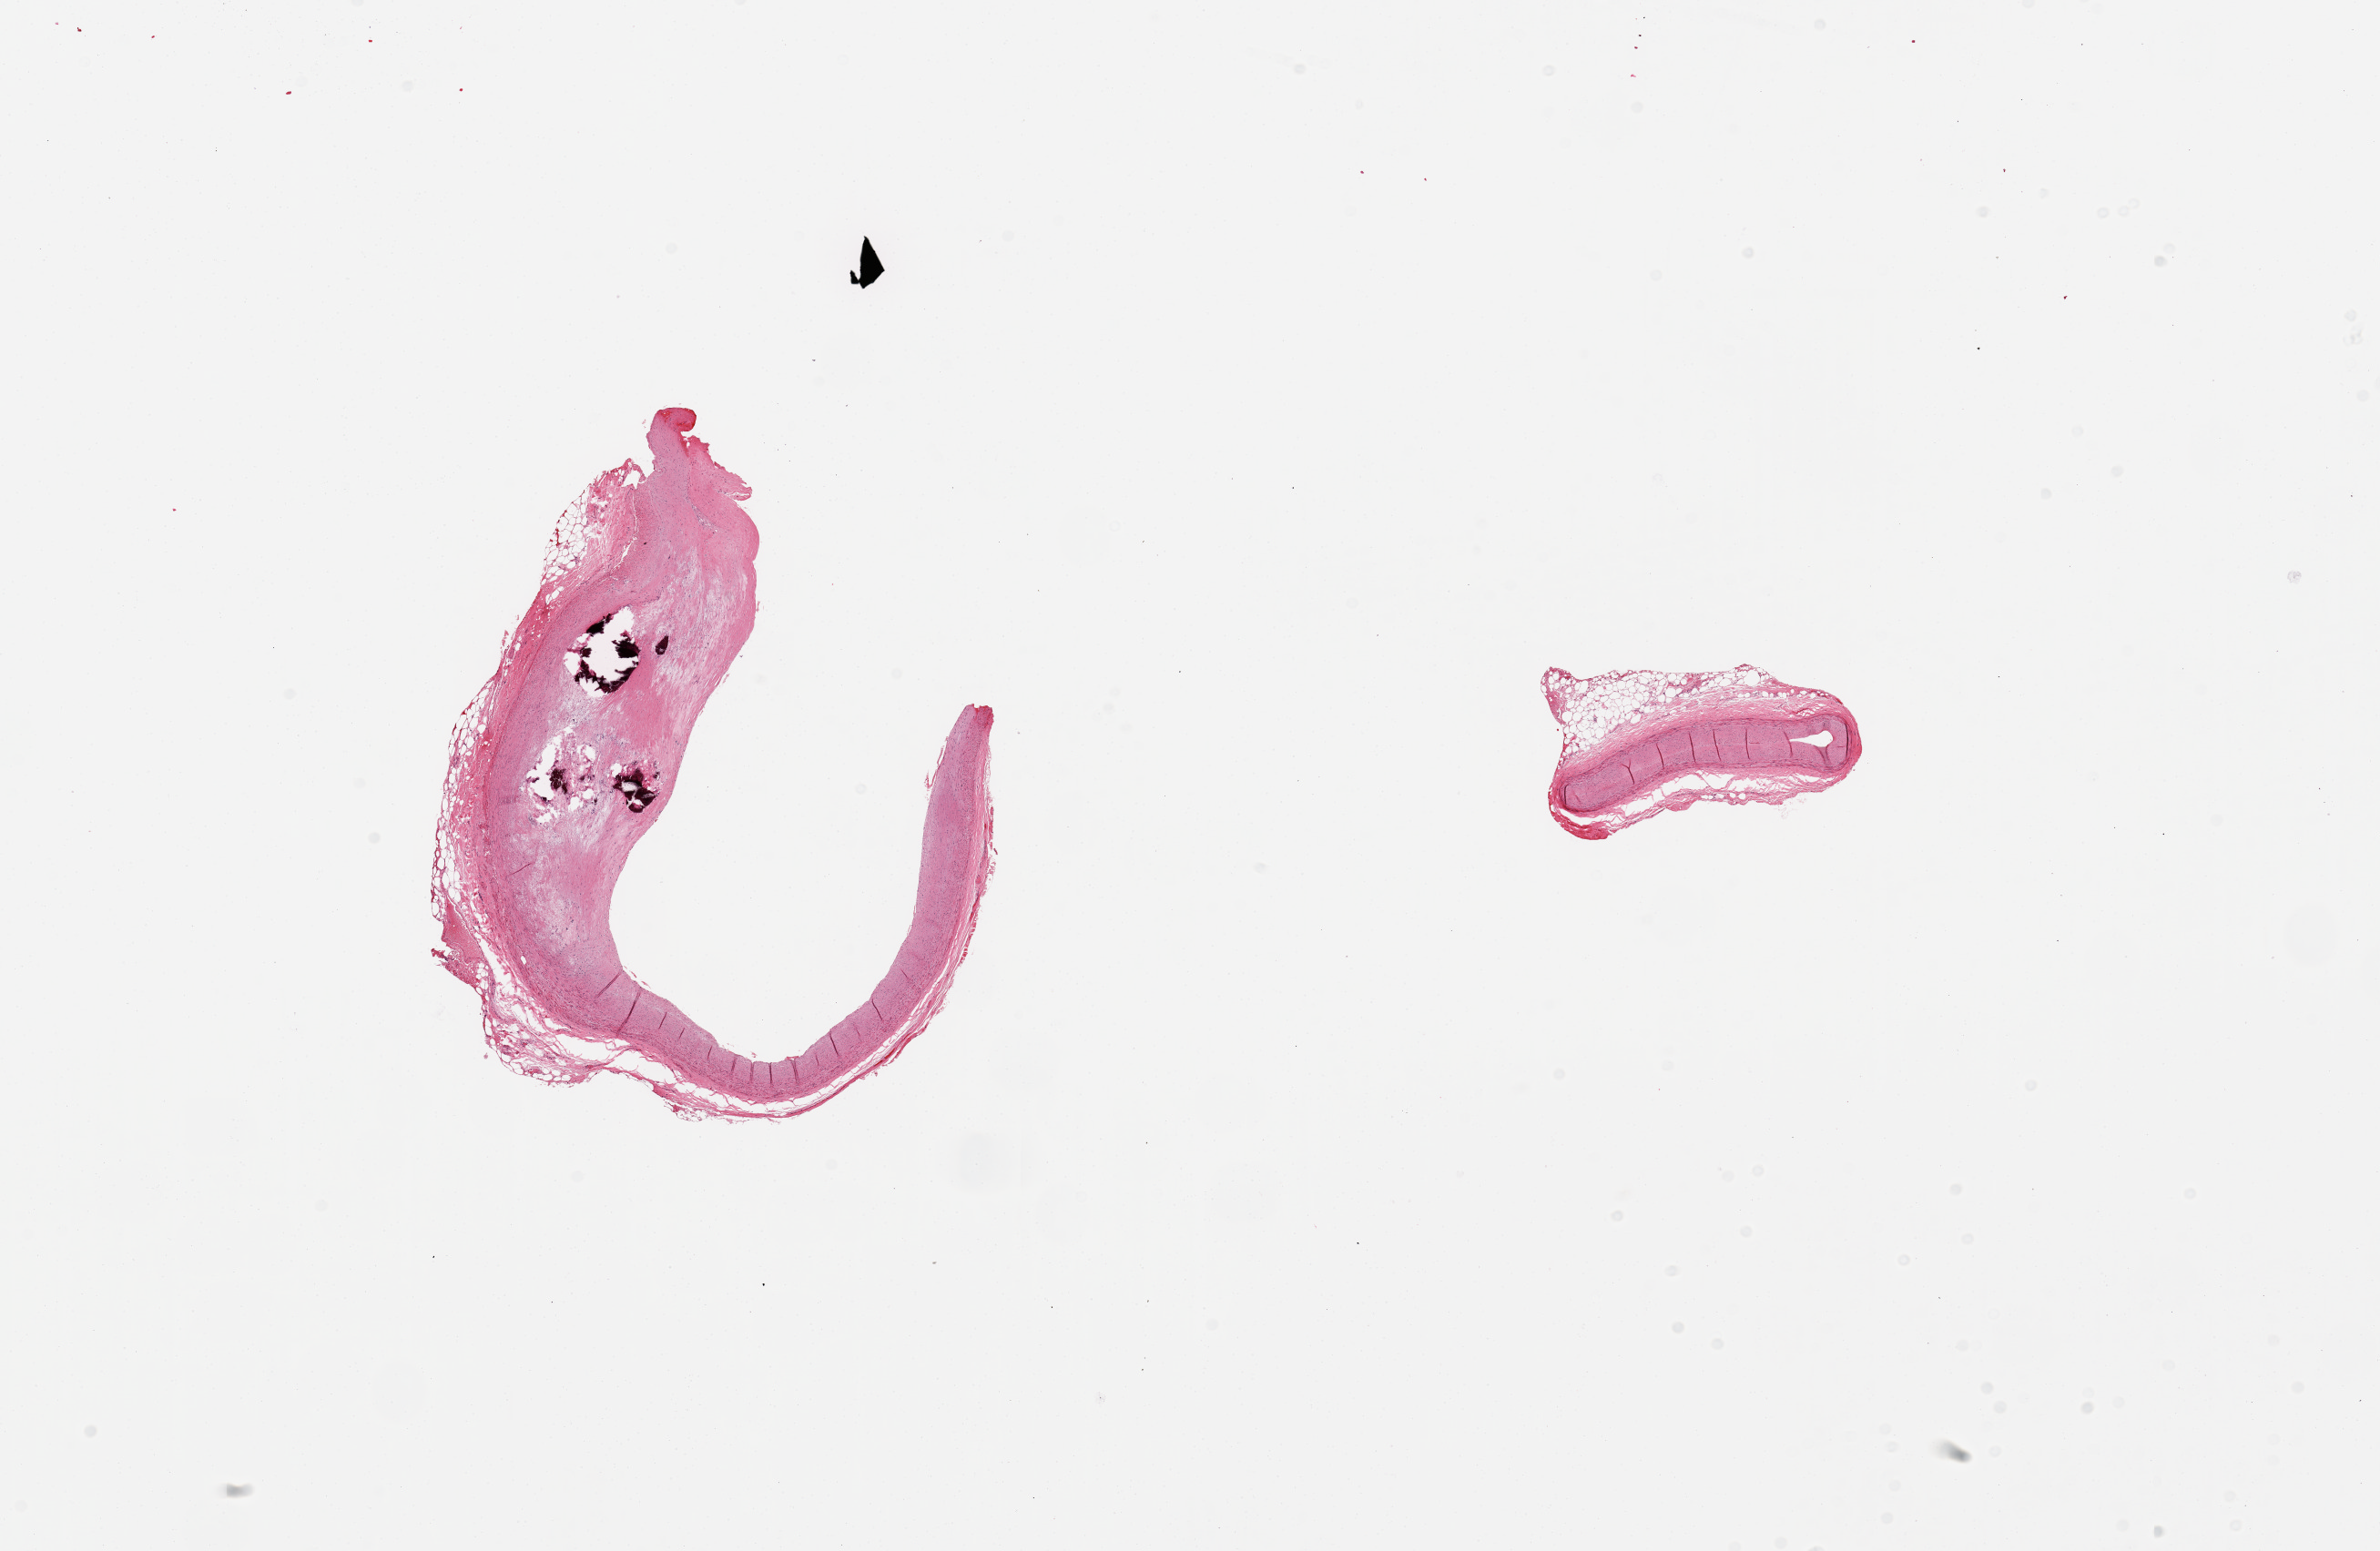
Hematoxylin and eosin (H&E) whole-slide image — shown as a low-resolution overview of the whole scanned area (about 20.7 x 13.5 mm); PAXgene-fixed, paraffin-embedded tissue; target tissue: coronary artery; tissue donor sample. Donor: male.
Reviewer comment on this tissue sample: 2 pieces; large piece contains heavily calcified atheromatous plaque (over 50% area); smaller piece has 40% external fat.